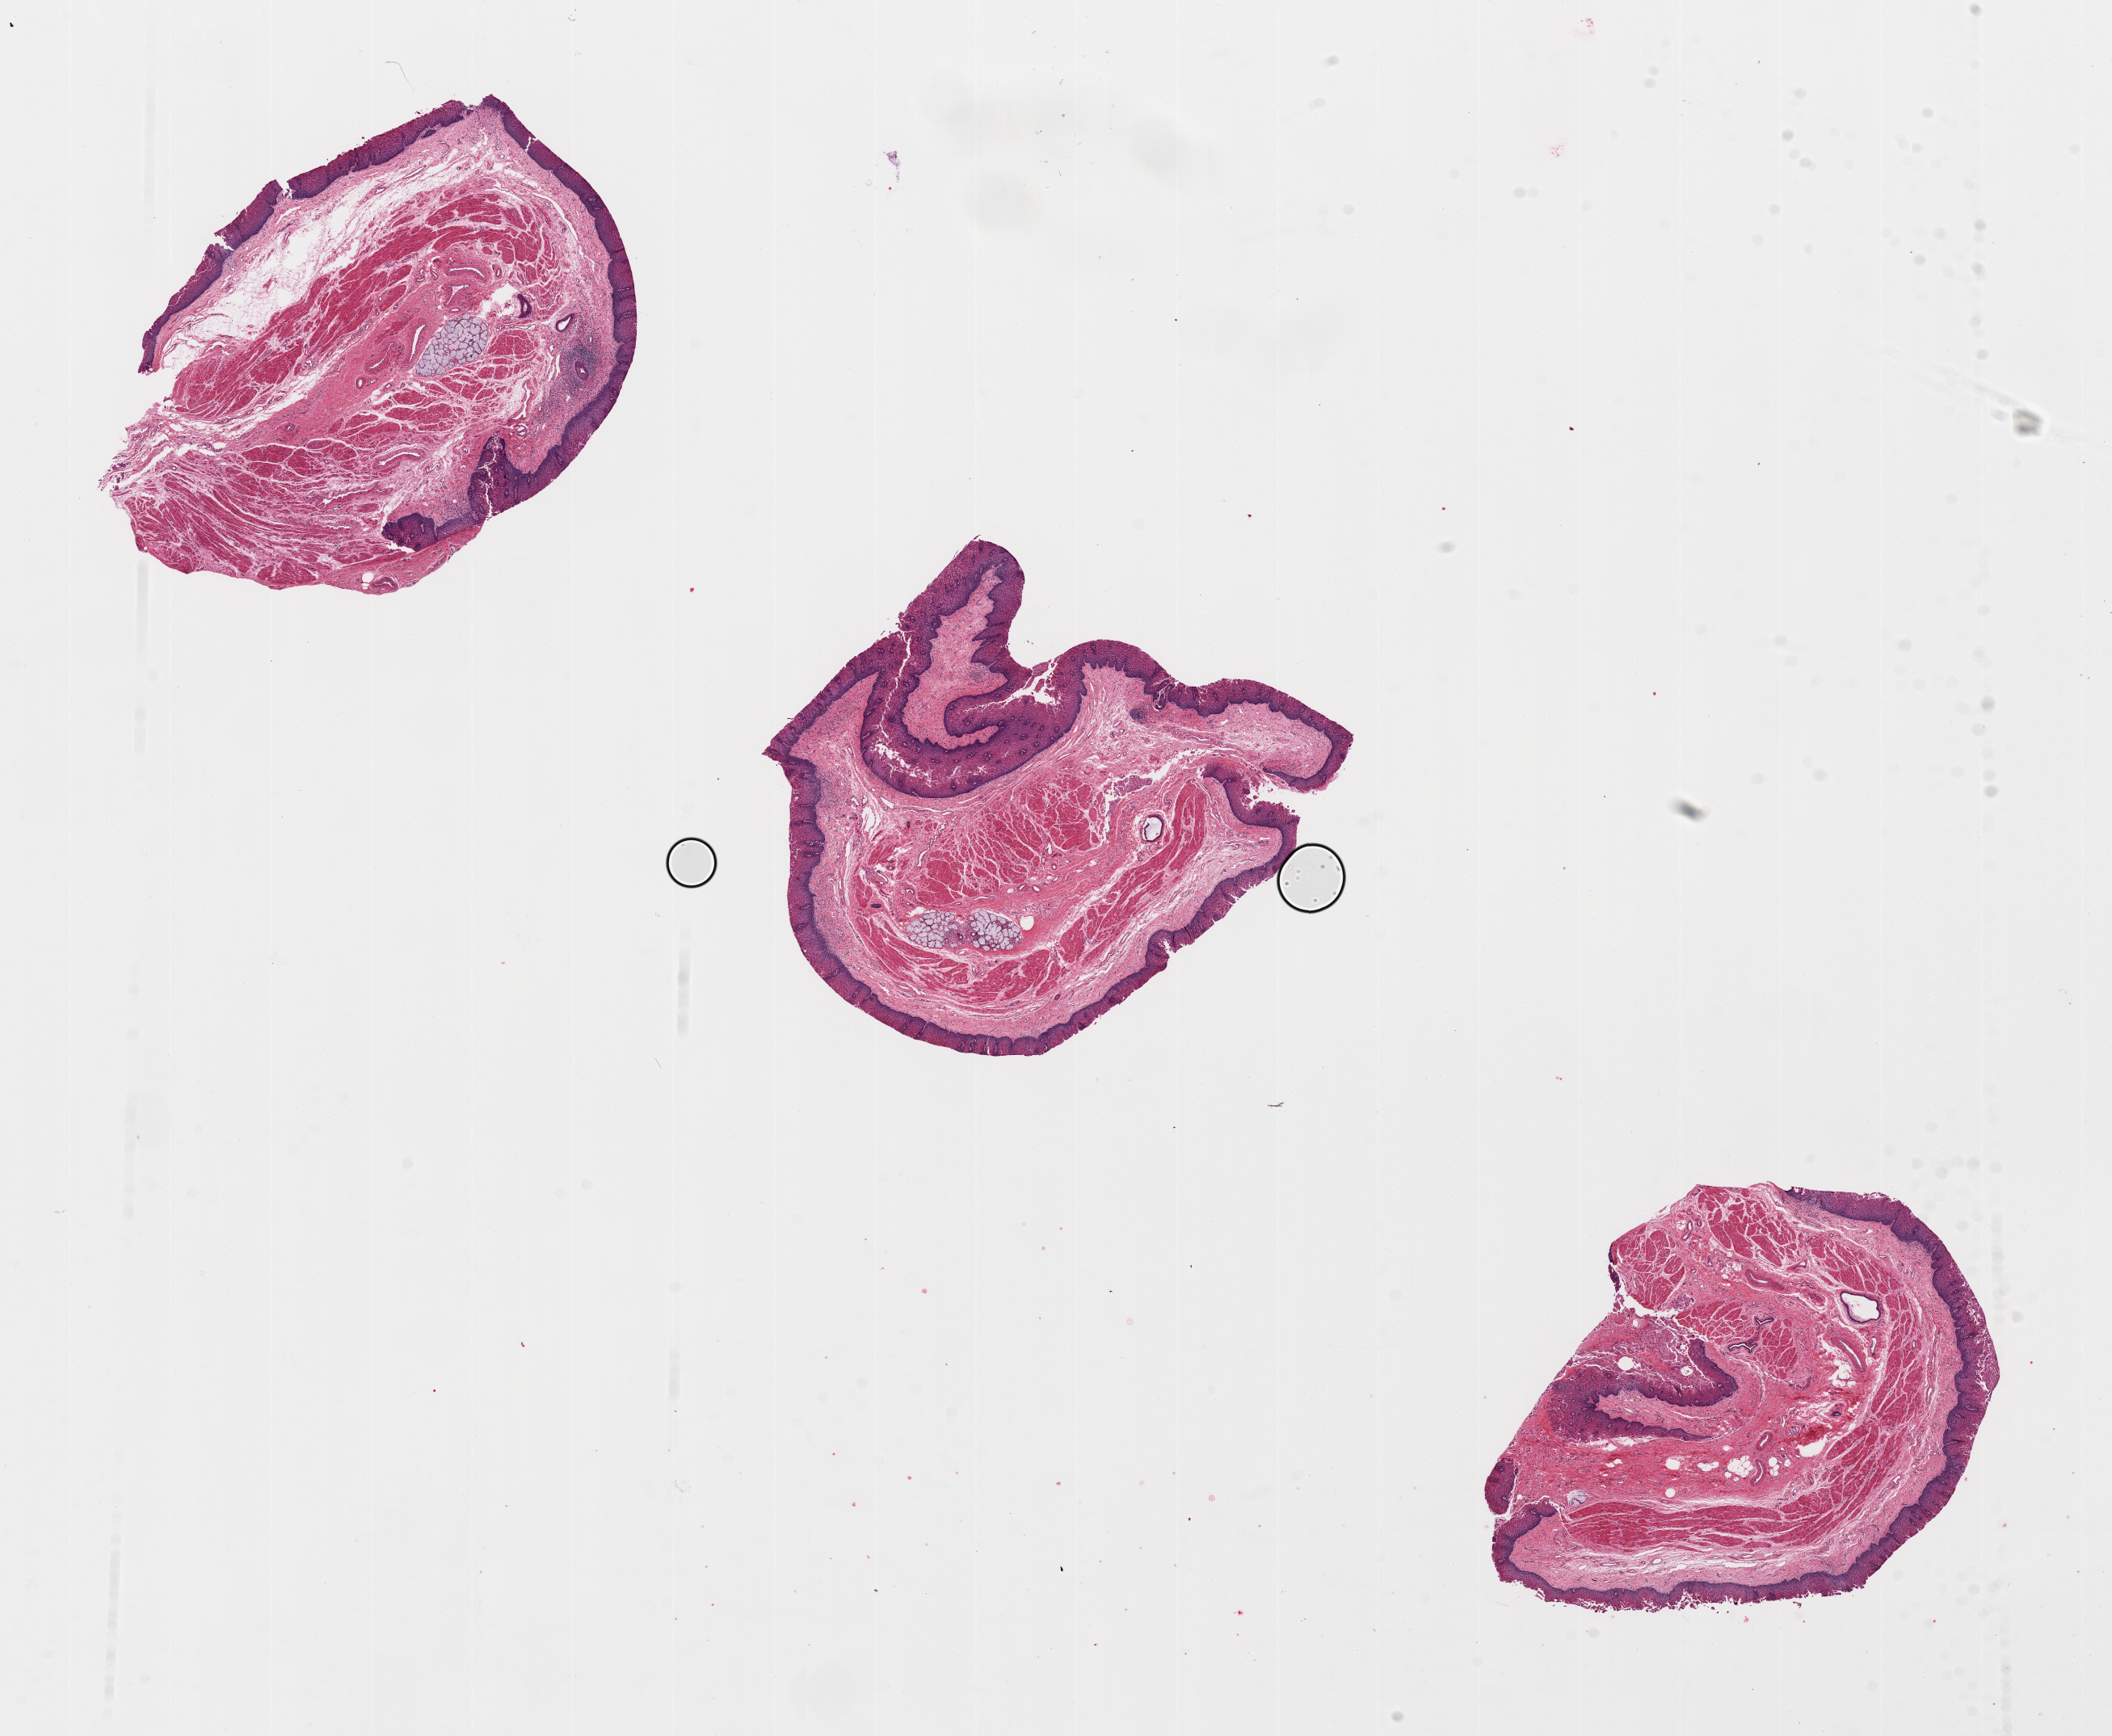
Digitized hematoxylin and eosin (H&E)-stained section, brightfield — whole scanned area (about 20.7 x 17.0 mm) shown as a low-resolution overview, PAXgene-fixed, paraffin-embedded tissue, sampled site (target tissue): esophageal mucous membrane, donor tissue sample. Donor: male.
Reviewer comment on this tissue sample: Well preserved squamous epithelium. 5.5x3.8mm.